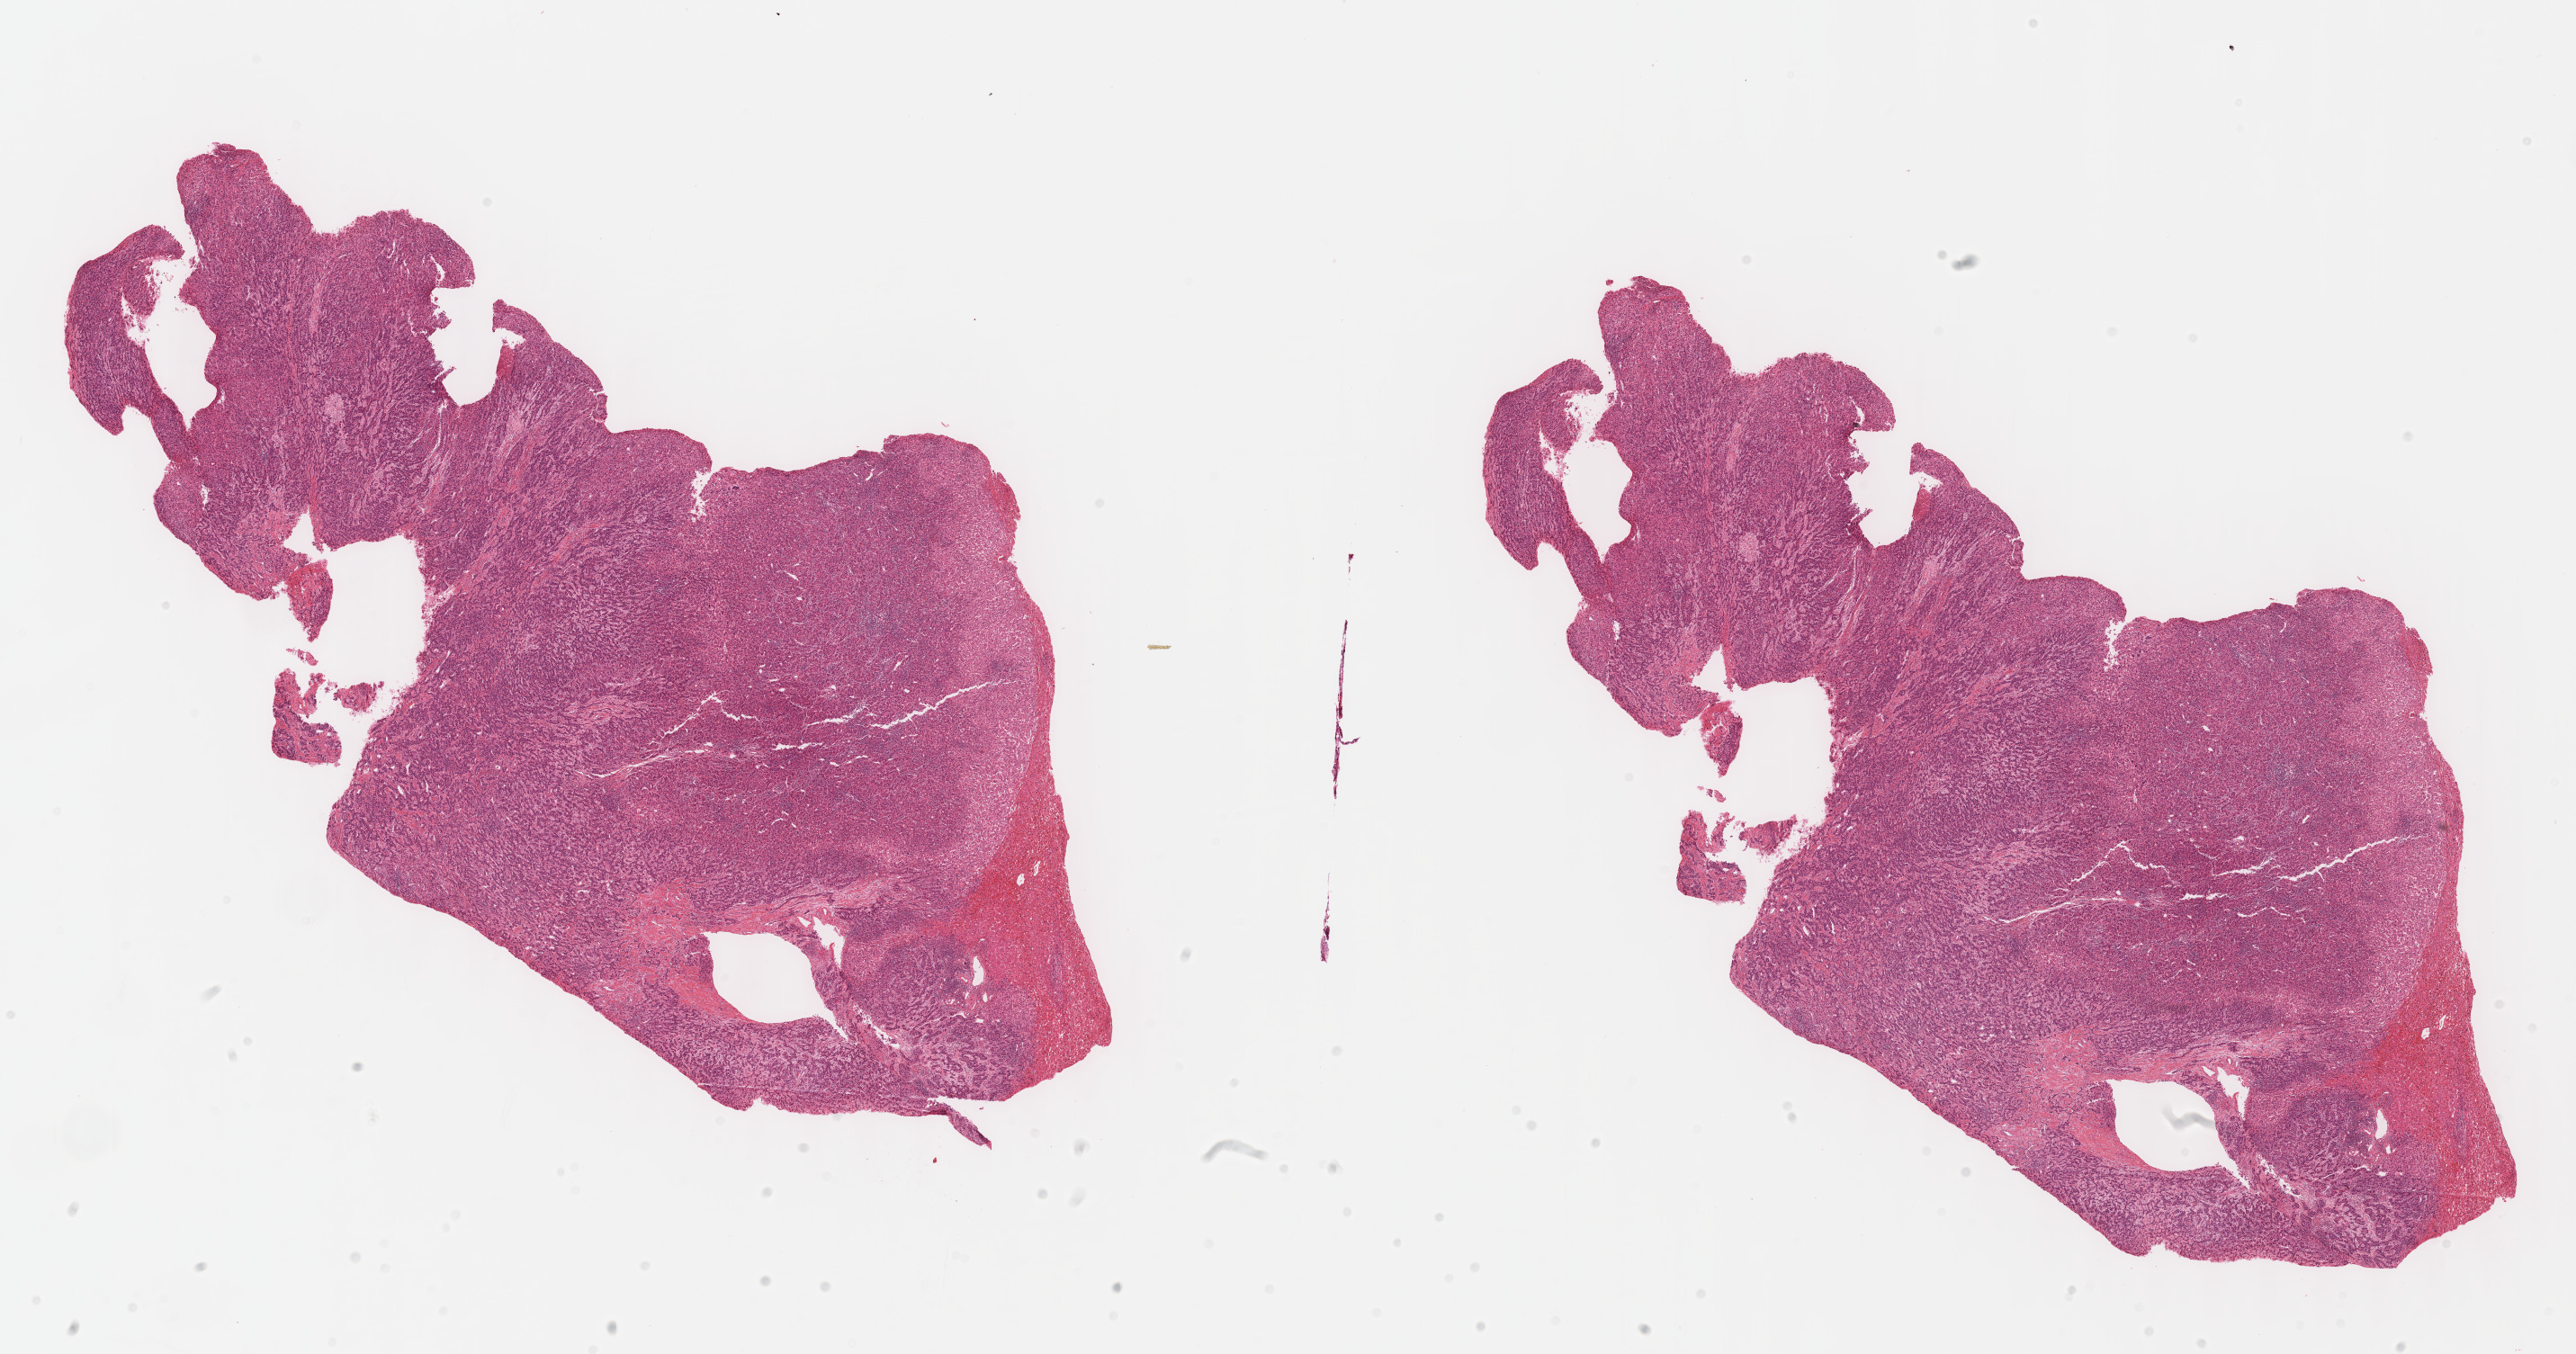
Whole-slide histology image, Hematoxylin and eosin (H&E) stained — low-resolution overview of the scanned area, about 23.1 x 12.2 mm (slide scanned at 40x), formalin-fixed paraffin-embedded (FFPE) diagnostic section, liver, primary tumour sample. Female patient; age at initial diagnosis 43 years. Histologic grade: G3 (poorly differentiated).
Pathologic diagnosis: Hepatocellular carcinoma, NOS. AJCC pathologic stage: I.